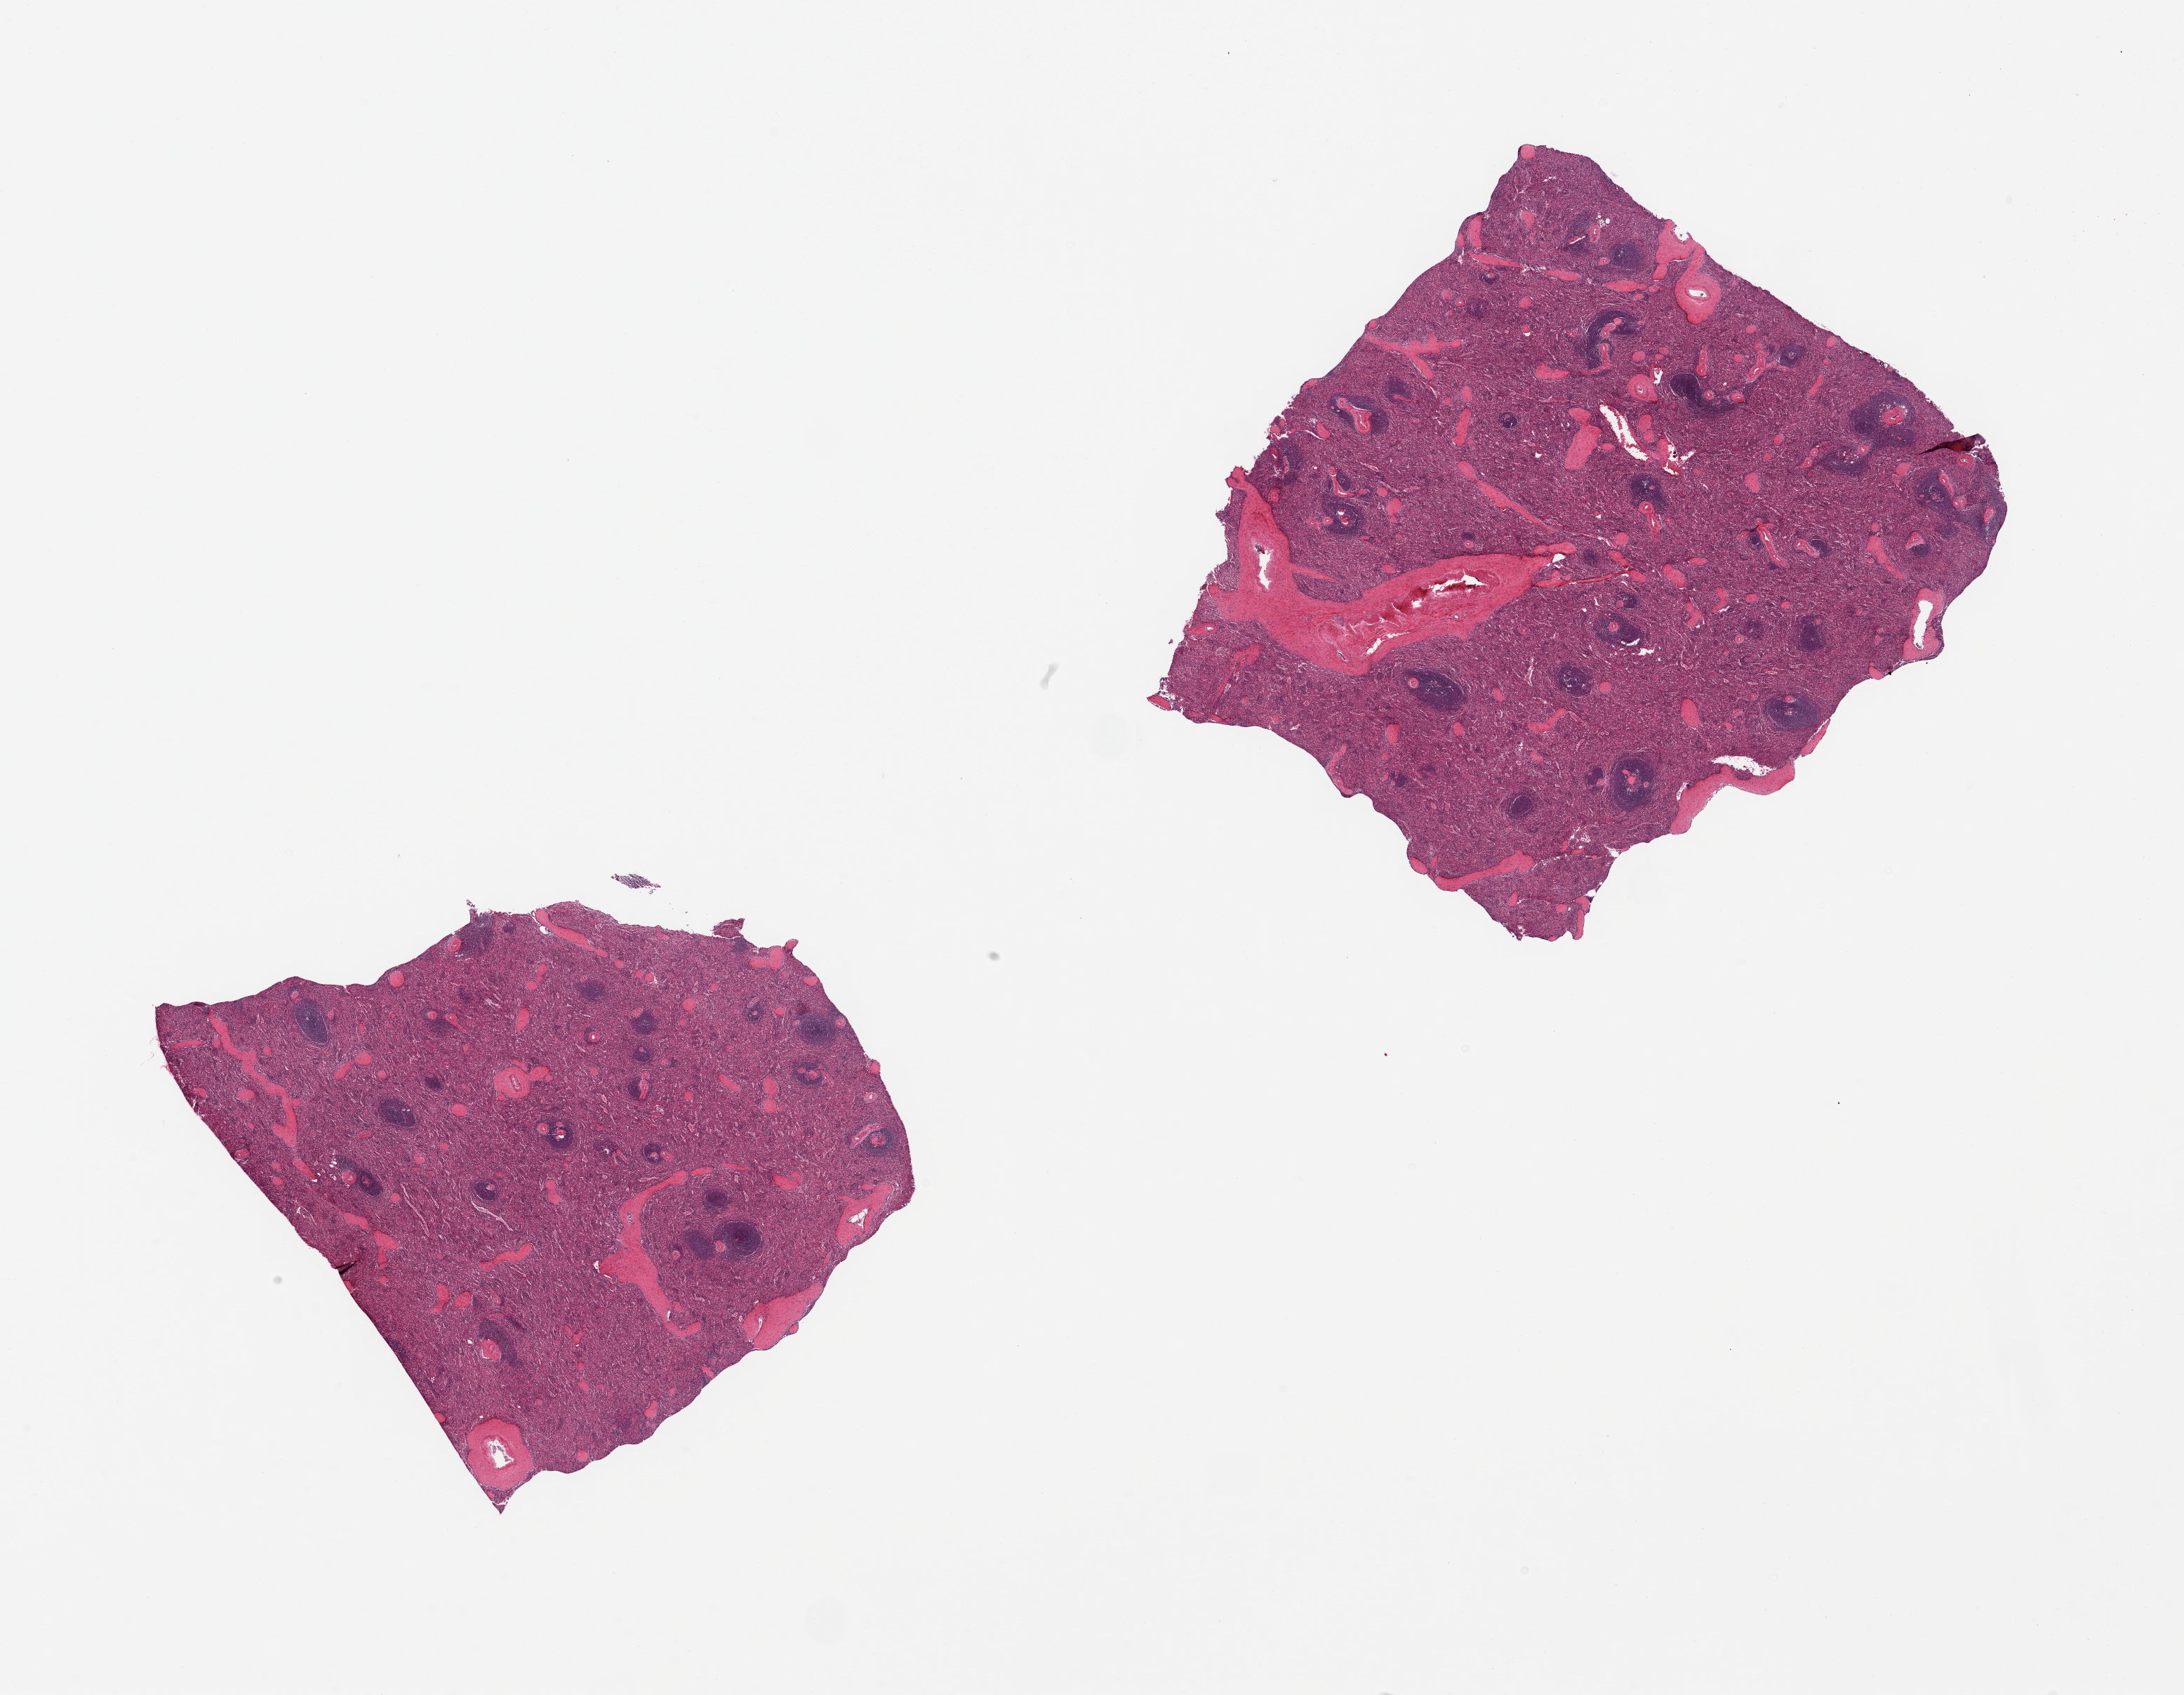
Digitized haematoxylin and eosin-stained section — shown as a low-resolution overview of the whole scanned area (about 24.6 x 19.1 mm); PAXgene-fixed, paraffin-embedded tissue; target tissue: spleen; donor tissue sample. Donor: male.
• pathologist's review note for this sample: 2 pieces; lymphoid tissue not abundant; no congestion